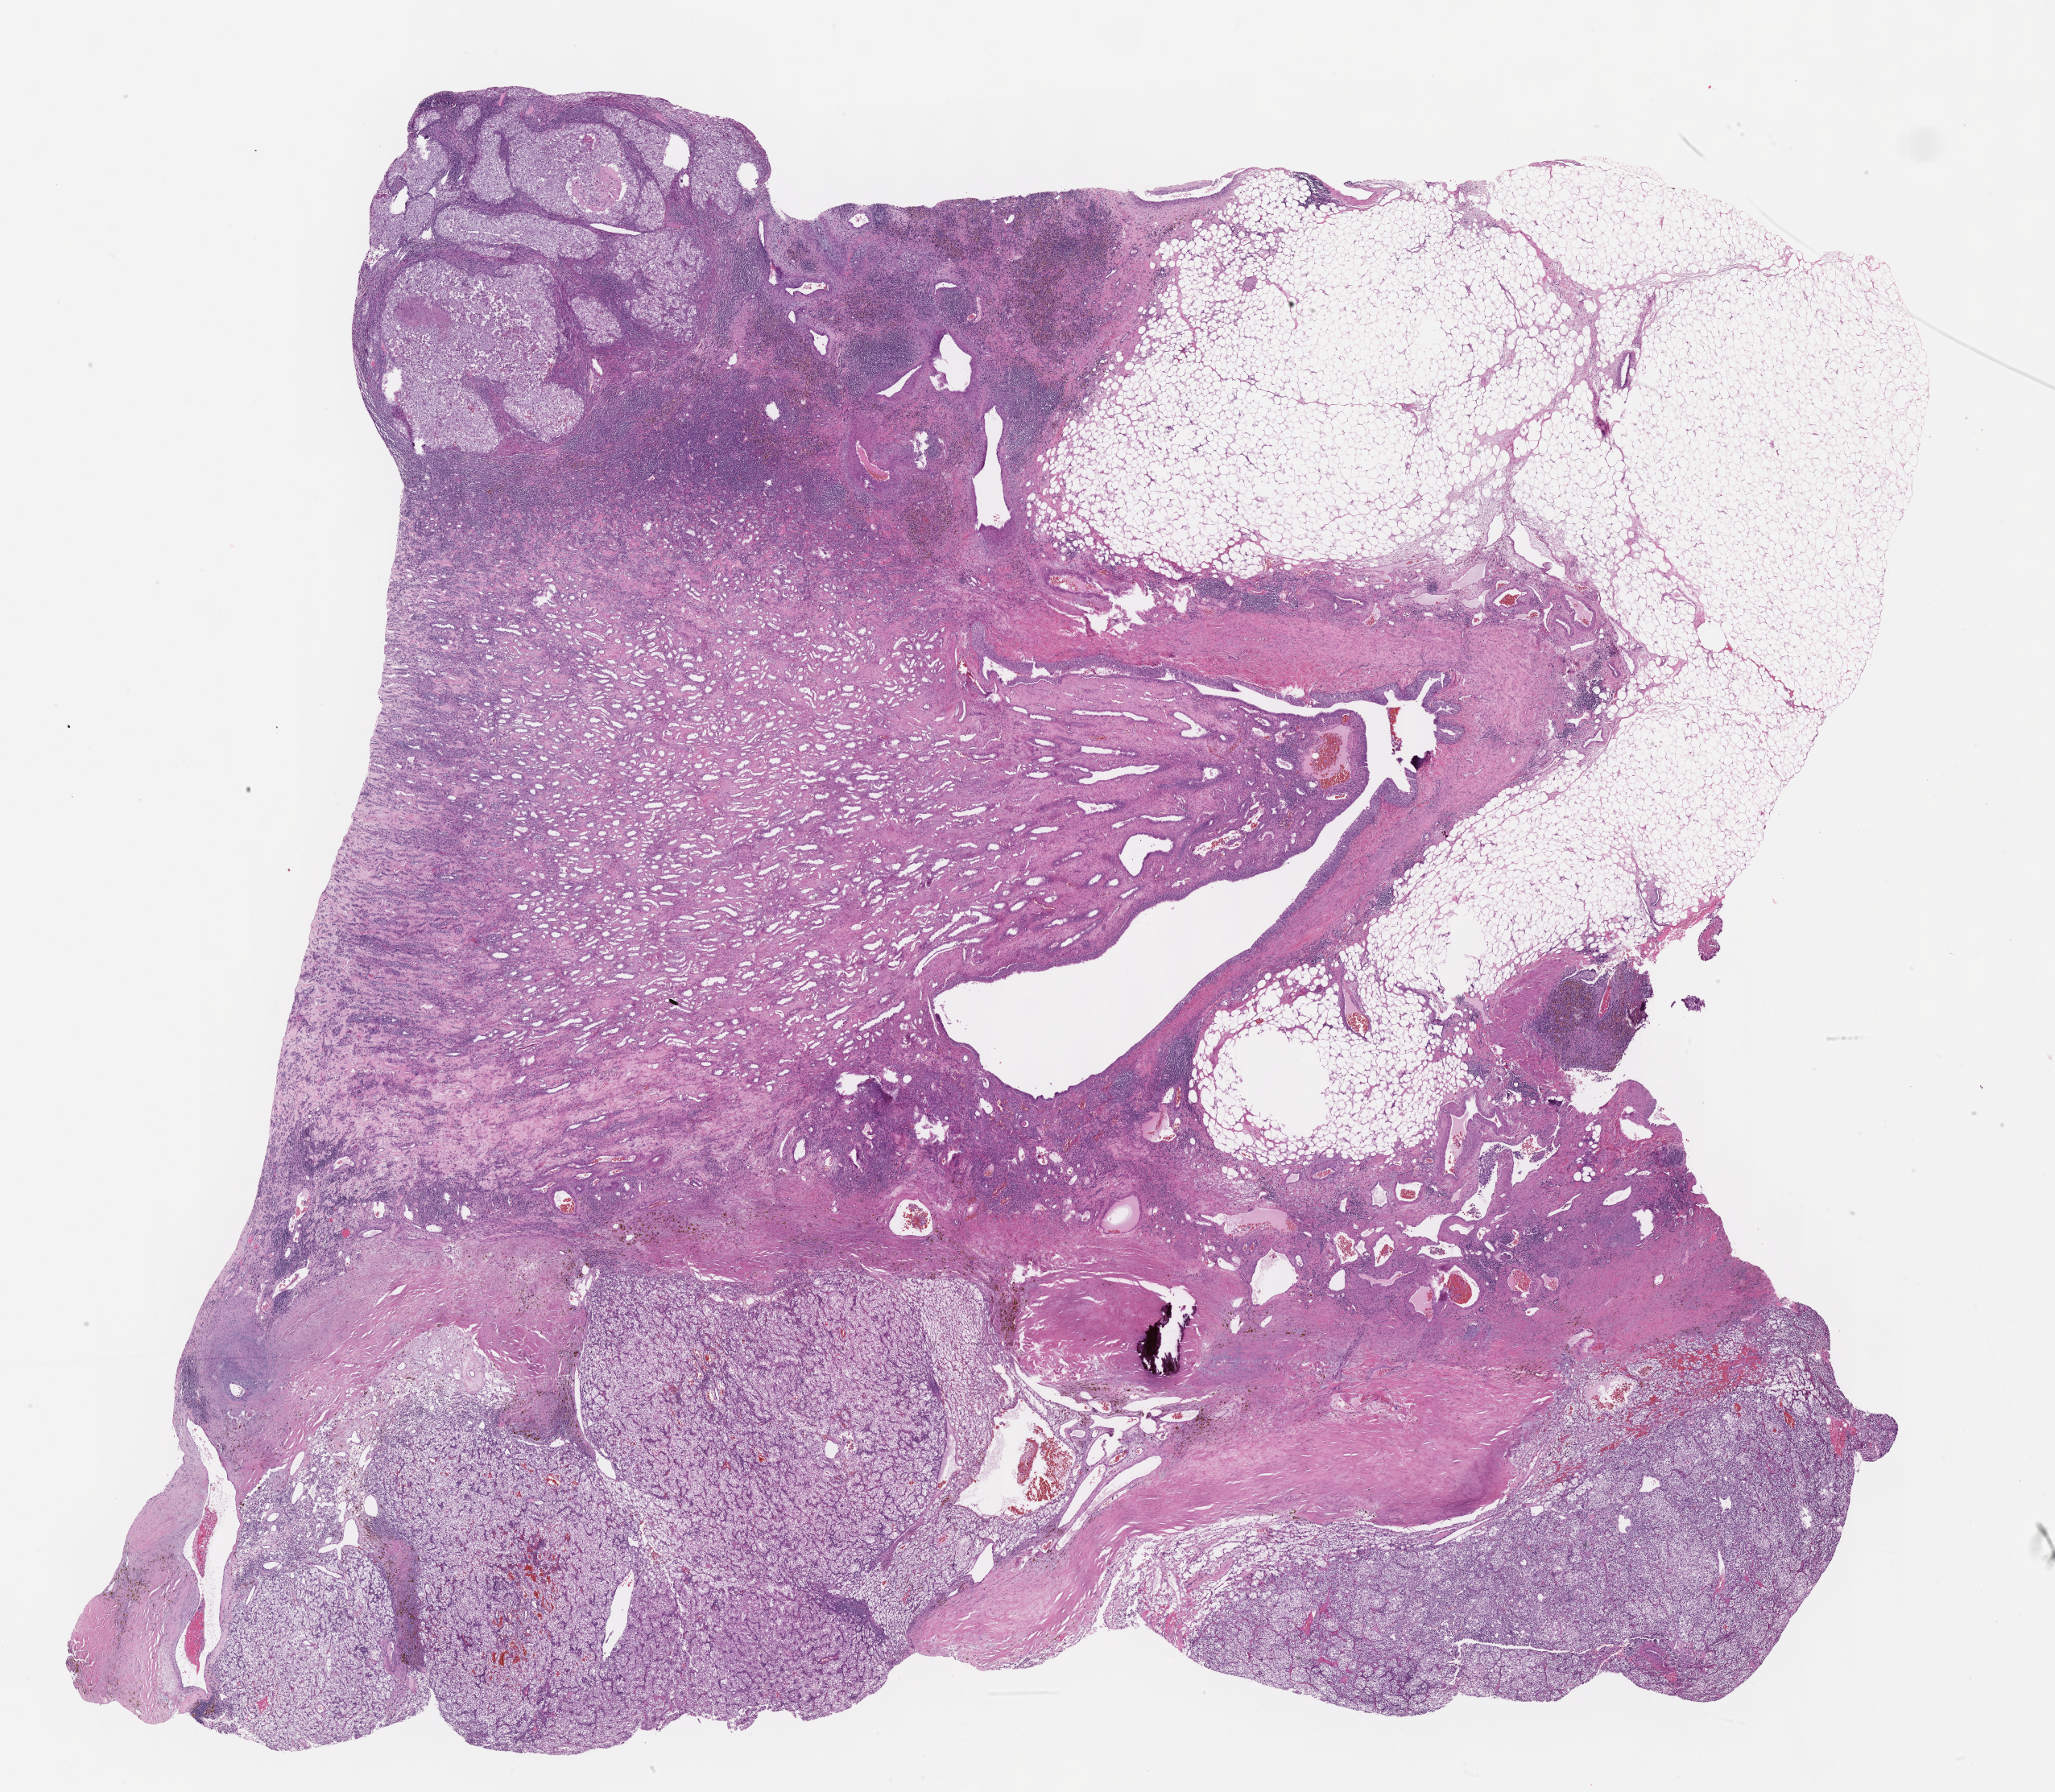
H&E-stained whole-slide image, low-resolution overview of the scanned area, about 20.6 x 18.0 mm; formalin-fixed paraffin-embedded (FFPE) diagnostic section; primary tumour sample from the kidney. Patient: male, age at initial diagnosis 64 years. Histologic grade: G4 (undifferentiated).
Histologic diagnosis: Clear cell adenocarcinoma, NOS. AJCC pathologic stage: IV. Laterality: left.